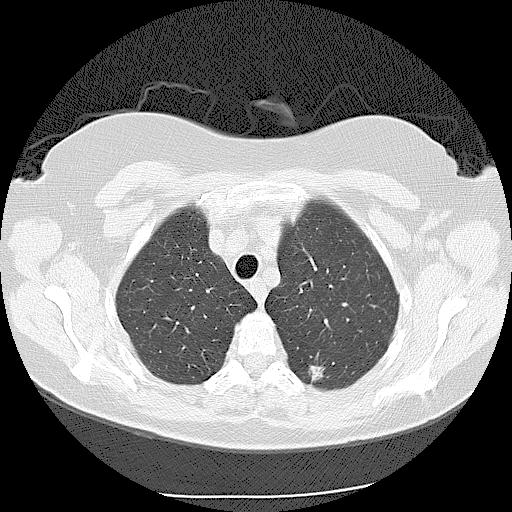
Low-dose screening chest CT, one axial slice; position 91 of 116 along the scan axis; reconstruction kernel LUNG; 120 kVp; lung window (W 1500 / L -600 HU); 2.5 mm slice thickness; 512 × 512 image matrix, field of view 360 × 360 mm.
Annotated regions visible in this slice (outlined manually by an expert reader):
- lesion 1 (tumor, lower lobe of left lung): bounding box <308,365,325,382> (left, top, right, bottom; pixels)